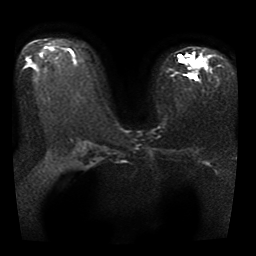
Breast MRI, one axial slice; position 22 of 41 along the scan axis; diffusion-weighted series; image 2 of 4 stored at this slice position (different b-values; order by instance number); 1.5 T; 5 mm slice thickness; 256 × 256 image matrix, field of view 330 × 330 mm. Female patient.
Outlined on this slice (outlined manually by an expert reader):
- tumour on diffusion-weighted imaging: bounding box [x1, y1, x2, y2] px = [178, 55, 200, 69]